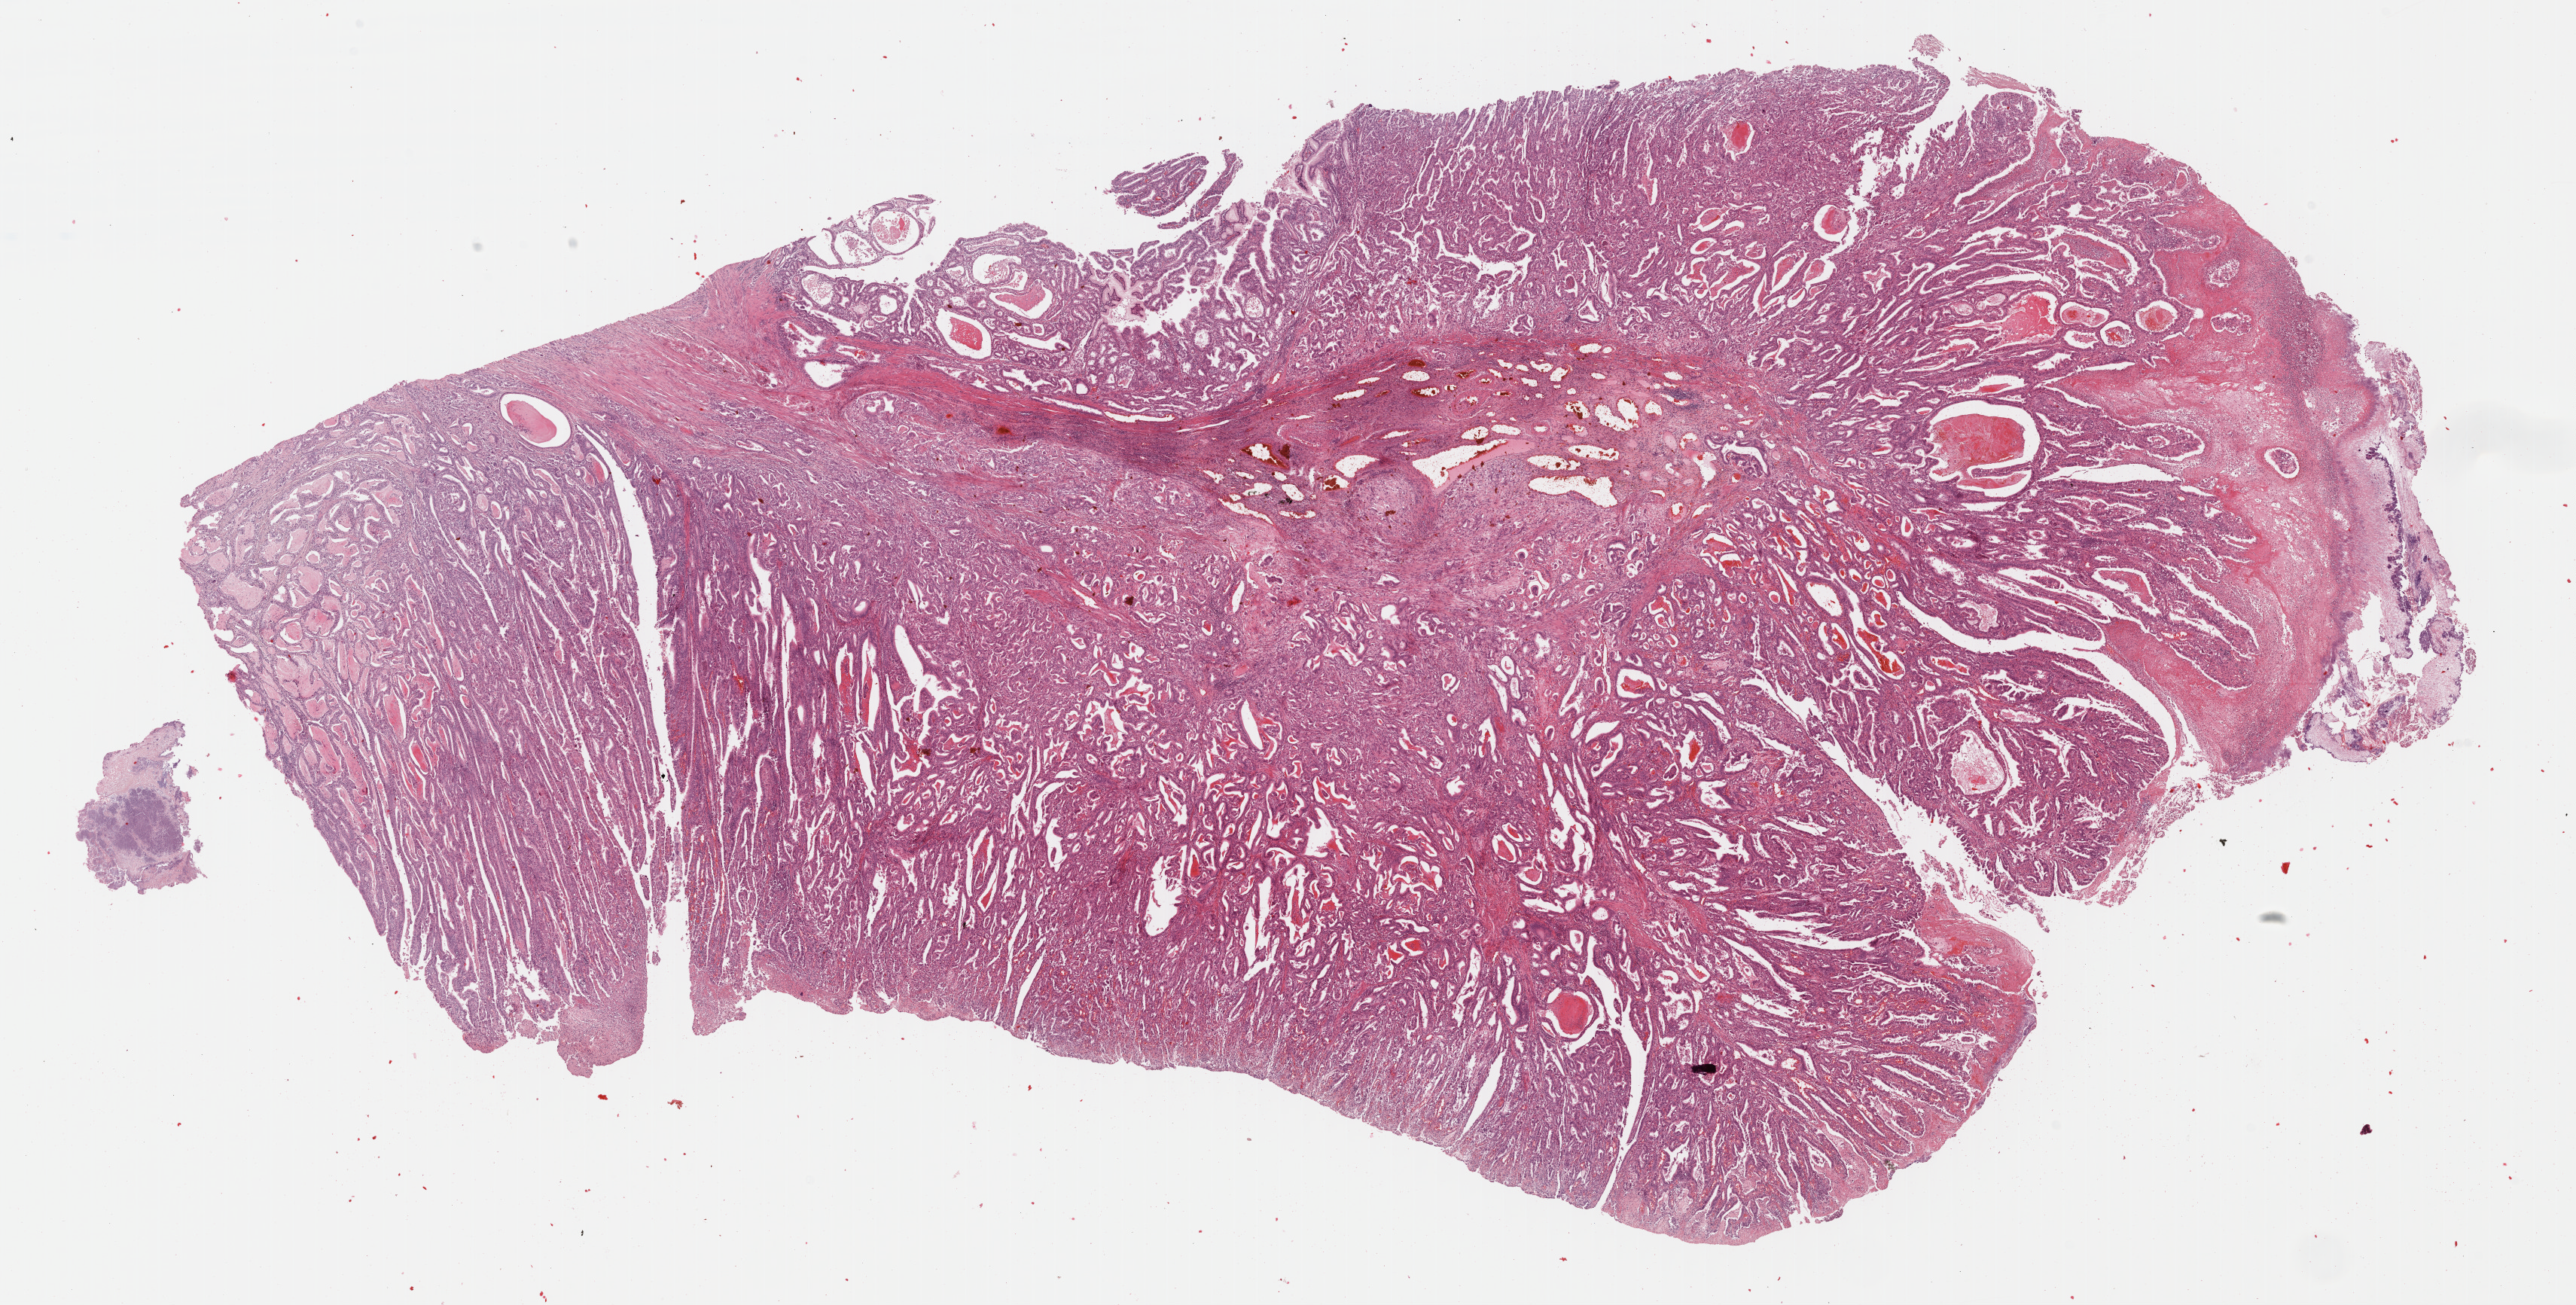
Whole-slide histology image, H&E — low-resolution overview of the scanned area, about 26.9 x 13.6 mm; formalin-fixed paraffin-embedded (FFPE) diagnostic section; stomach, primary tumour sample. Patient: male, age at initial diagnosis 64 years. Histologic grade: G2 (moderately differentiated).
AJCC pathologic stage: IIB (6th edition). Pathologic diagnosis: Tubular adenocarcinoma (body of stomach). Lymph nodes positive (case pathology): 5 of 14 examined.